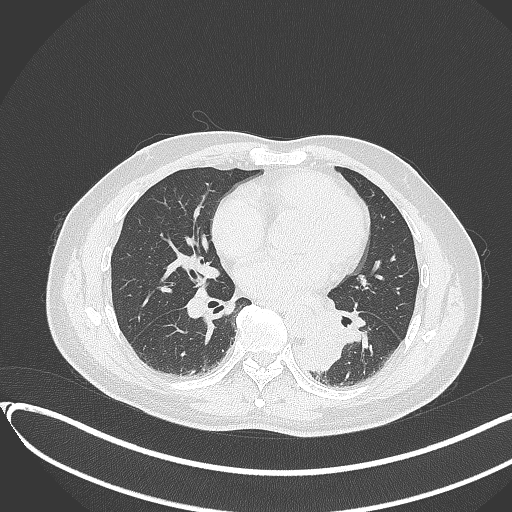
Chest CT, one axial slice. Slice 152 of 417 in the series (ordered by position). 120 kVp. Lung window (W 1500 / L -600 HU). 1 mm slice thickness. 512 × 512 image matrix. Male patient, age 54 years. Case-level facts recorded for this patient, not image findings: clinical TNM (as recorded): T3 N0 M0.
Structures marked on this image (bounding box drawn by a radiologist):
- lung tumour (recorded histology: squamous cell carcinoma): bounding box (x1, y1, x2, y2) in pixels: (292, 325, 343, 375)